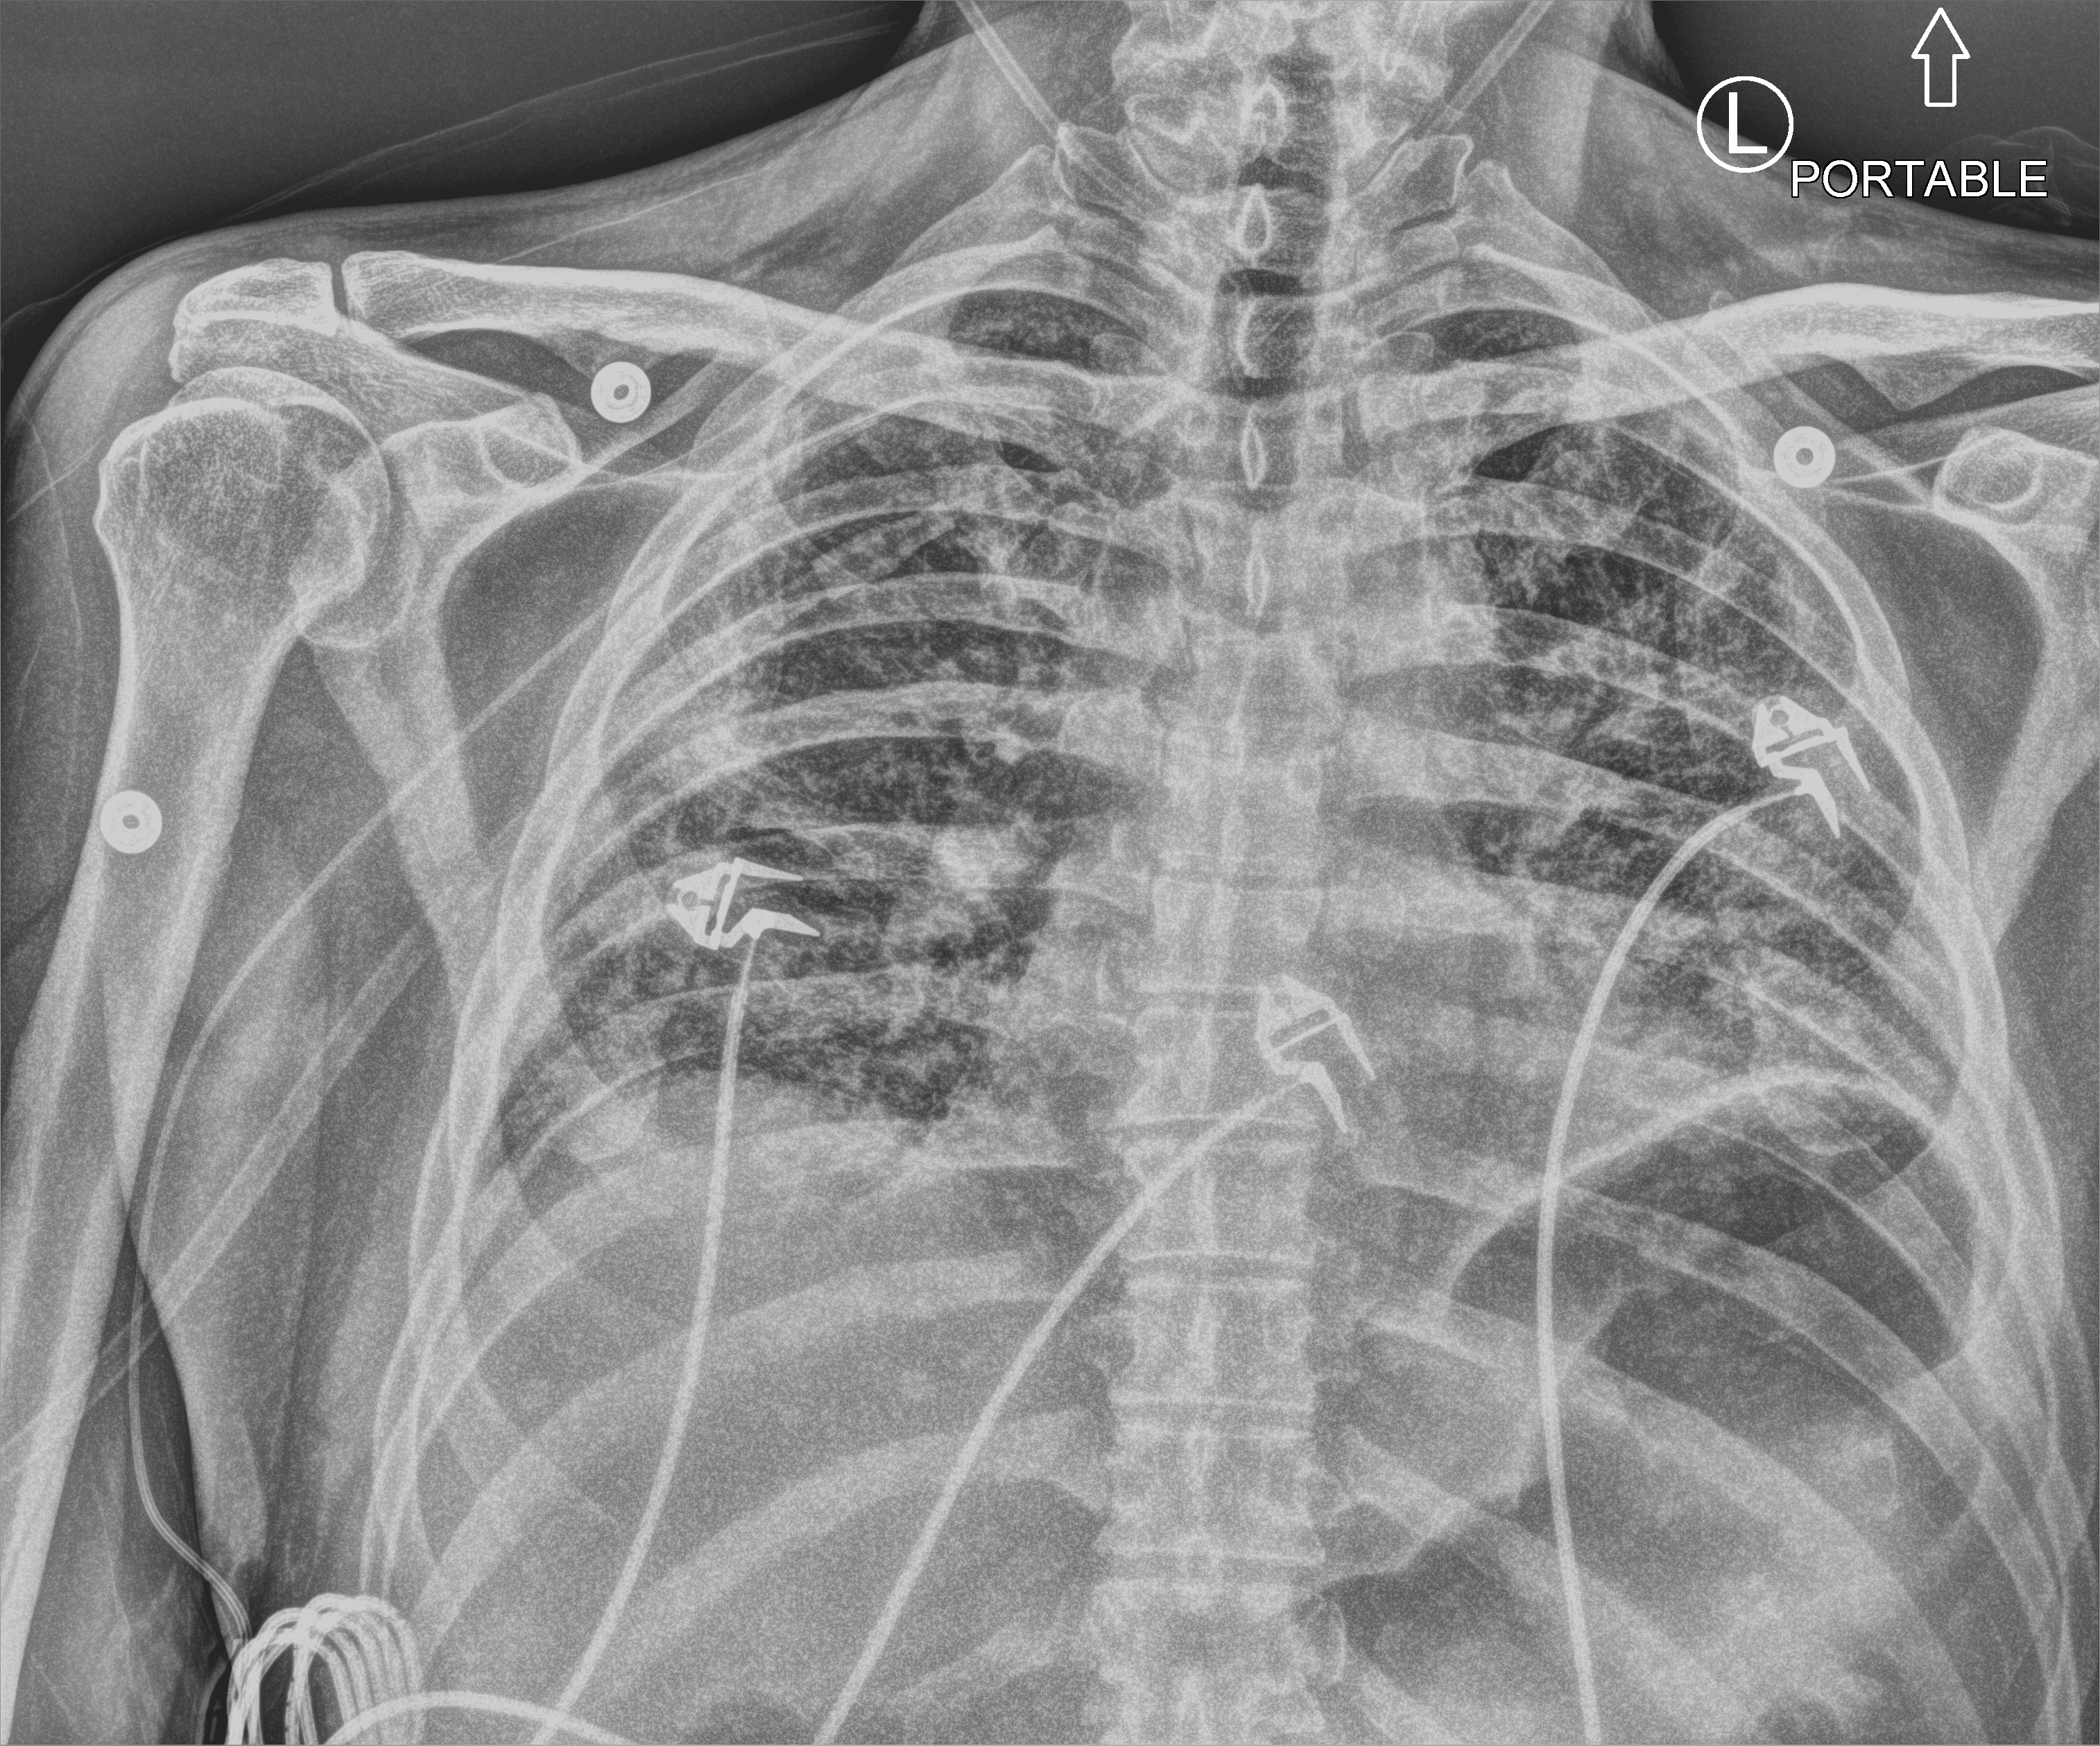
Portable chest radiograph. Male patient hospitalised with COVID-19, age 60–74 years.
From the hospital-stay record, not from the radiograph (when in the stay this image was taken is not recorded):
- chronic kidney disease (admission record): no
- admitted to intensive care during this hospital stay: yes